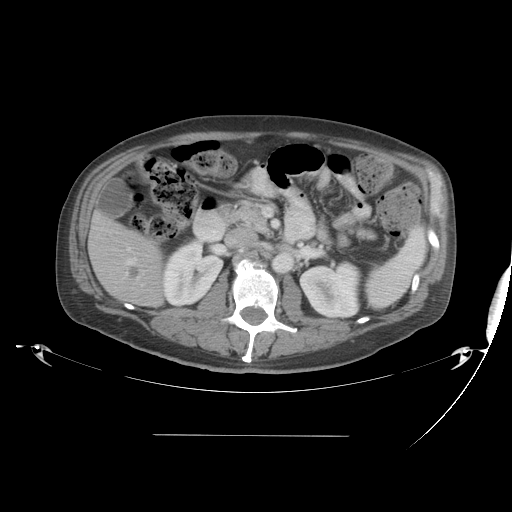
Contrast-enhanced abdominal CT, one axial slice; position 18 of 48 along the scan axis; reconstruction kernel STANDARD; intravenous contrast given; soft-tissue window (W 400 / L 40 HU); 5 mm slice thickness; 512 × 512 image matrix, field of view 486 × 486 mm. Male patient, age 65 years. Case-level facts recorded for this patient, not image findings: diagnosis: colorectal cancer liver metastases, imaged before liver resection; multiple liver metastases: yes; largest metastasis: 11 cm; disease in both lobes: yes.
Structures marked on this image (outlined manually by an expert reader):
- hepatic veins: box from (x=127, y=259) to (x=135, y=264) px
- liver: (x=90, y=215)–(x=165, y=306)
- portal vein (with intrahepatic branches): (x=98, y=235)–(x=143, y=286)
- liver metastasis: (x=128, y=267)–(x=139, y=279)